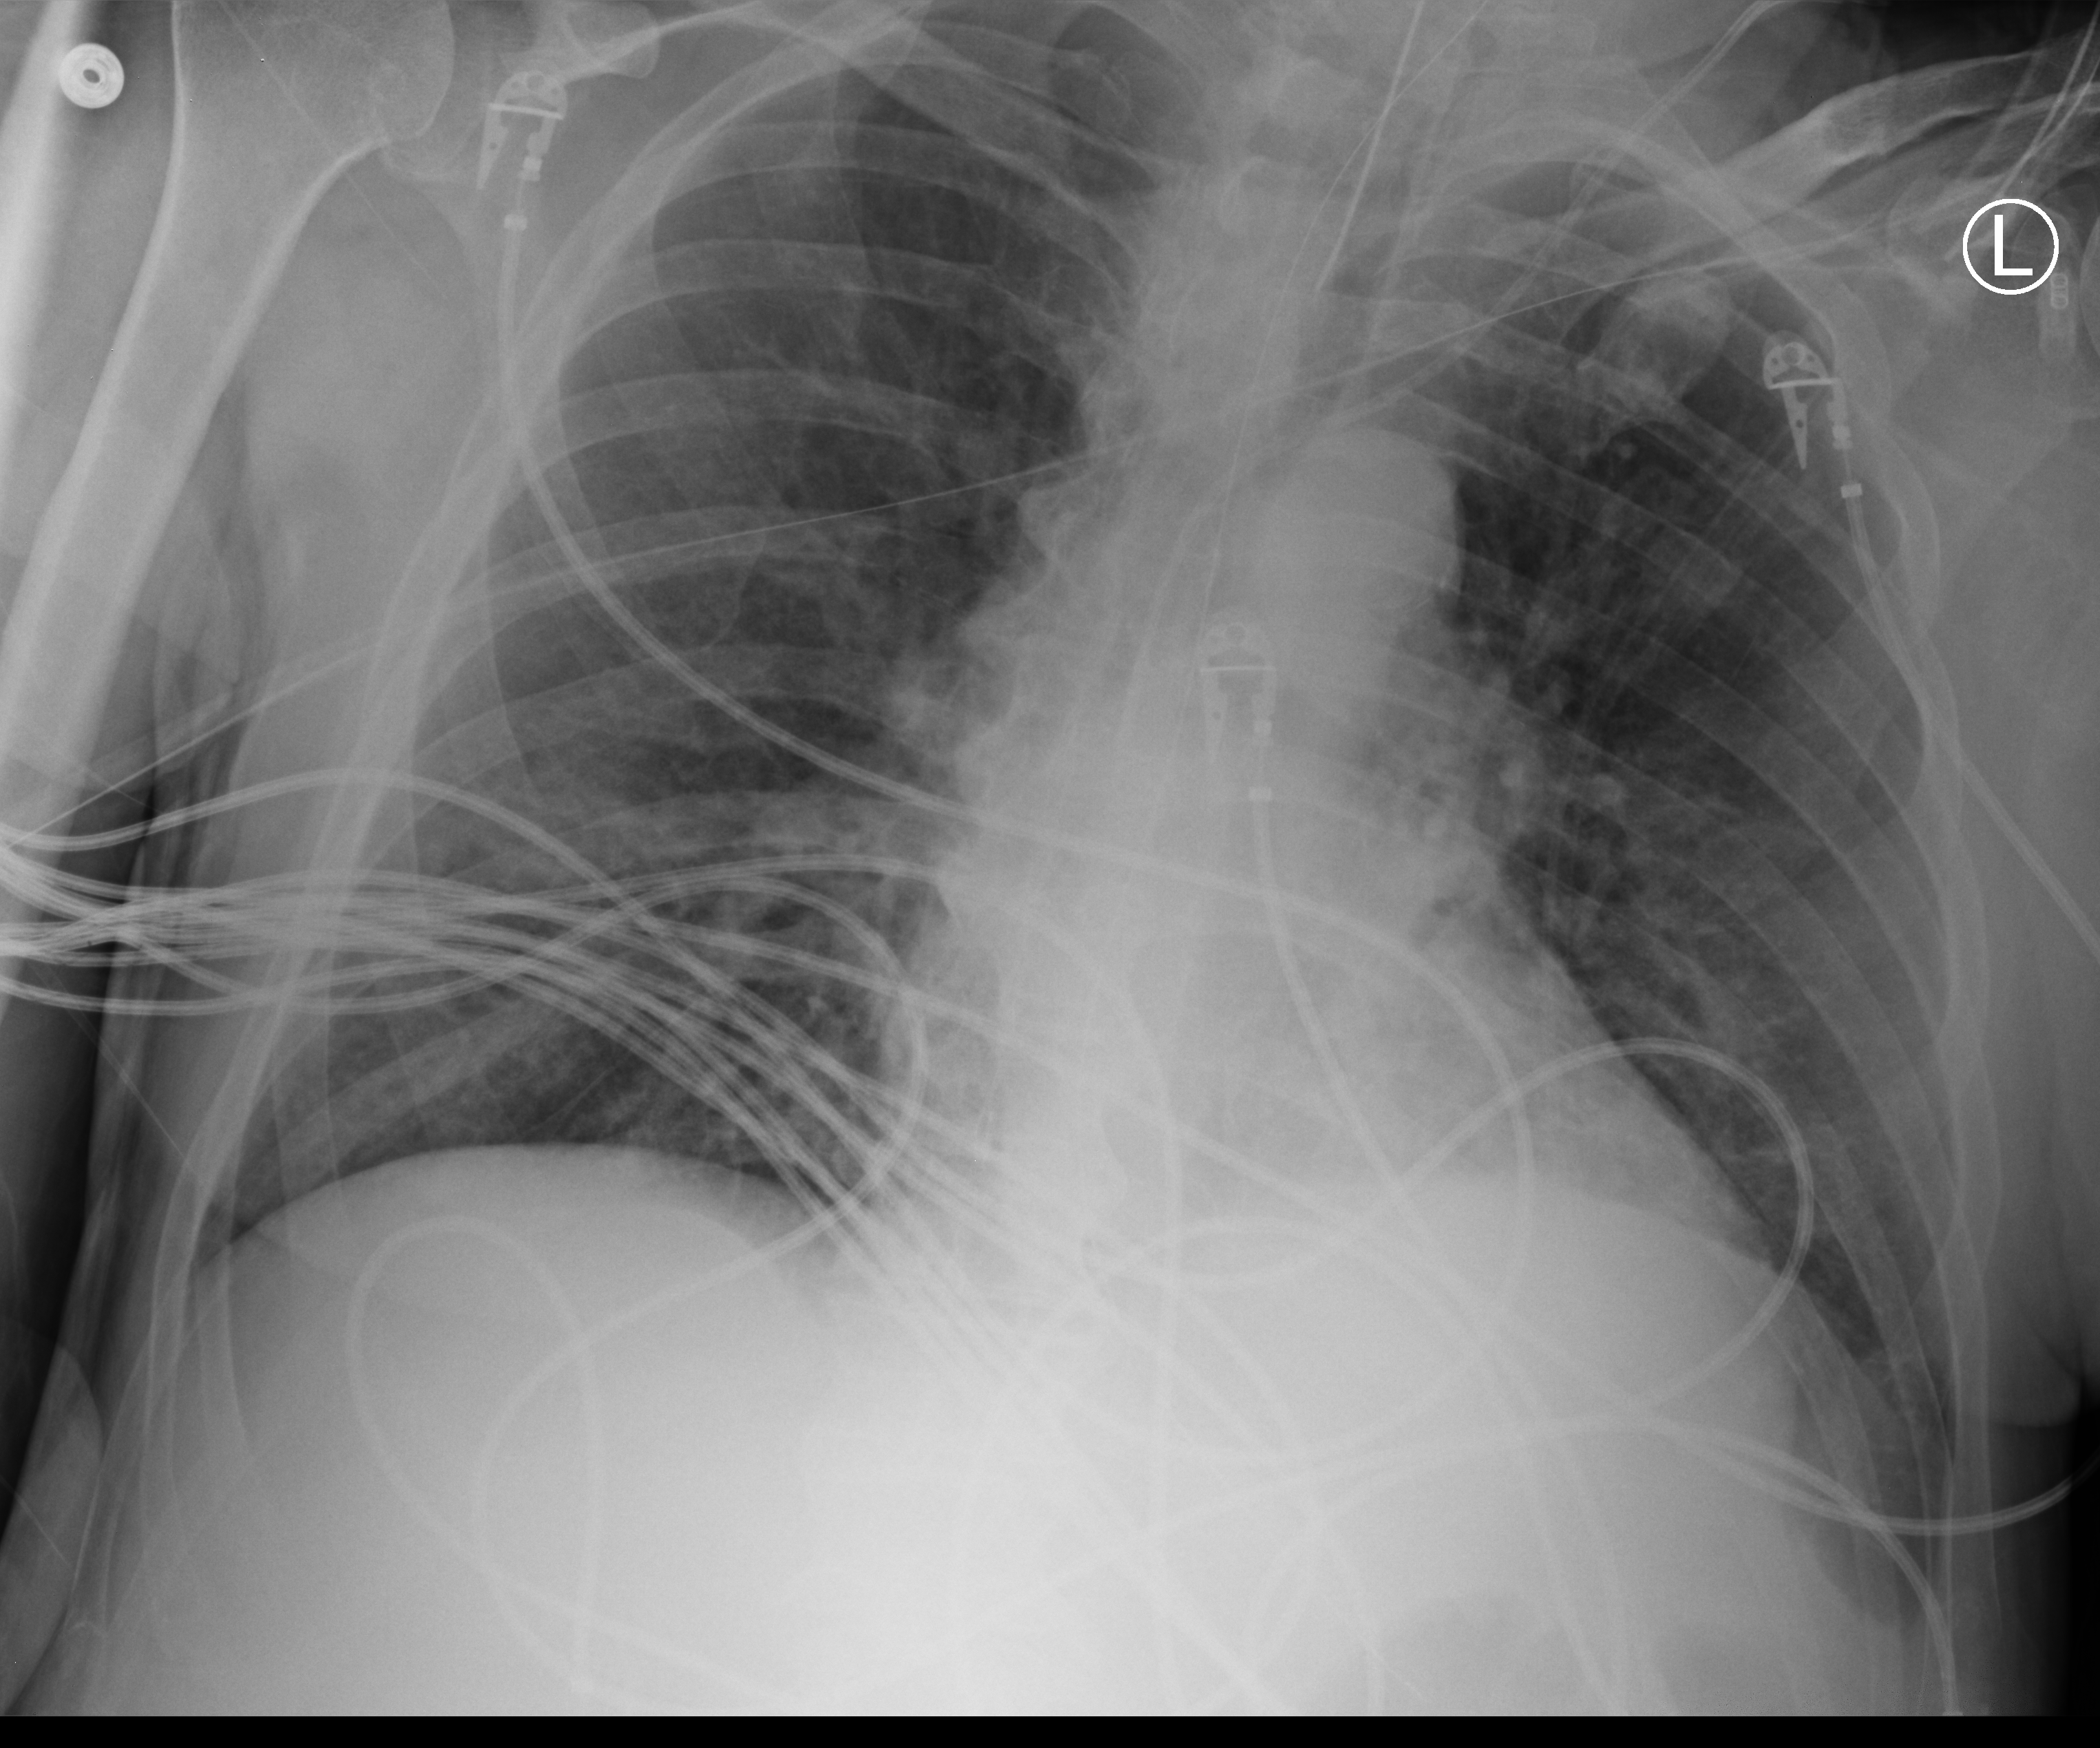
Bedside chest radiograph (computed radiography), anteroposterior (AP) projection. Male patient hospitalised with COVID-19, age 60–74 years.
Hospital-stay facts (about this admission, not read from this image; timing relative to this image not recorded): hypertension (admission record): yes; other chronic lung disease (admission record): no; admitted to intensive care during this hospital stay: yes.